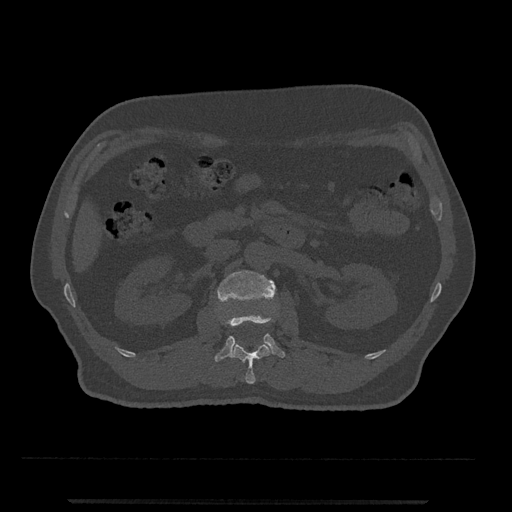
CT including the spine, one axial slice; slice 299 of 797 in the series (ordered by position); reconstruction kernel Br40s/3; bone window (W 1800 / L 400 HU); 512 × 512 image matrix. Male patient, age 63 years. Case-level facts recorded for this patient, not image findings: primary cancer: prostate.
Annotated regions visible in this slice (semi-automatic segmentation, software-assisted and operator-edited):
- L1 vertebra: bounding box <231,325,271,384> (left, top, right, bottom; pixels)
- L2 vertebra: <214,270,285,362>